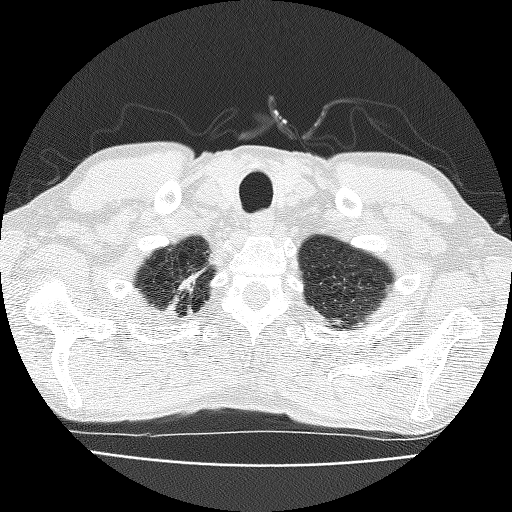
Low-dose screening chest CT, one axial slice; slice 163 of 185 in the series (ordered by position); reconstruction kernel FC51; lung window (W 1500 / L -600 HU); 512 × 512 image matrix.
Structures marked on this image (expert manual segmentation):
- lesion 1 (nodule, upper lobe of right lung): bounding box (x1, y1, x2, y2) in pixels: (179, 272, 201, 291)